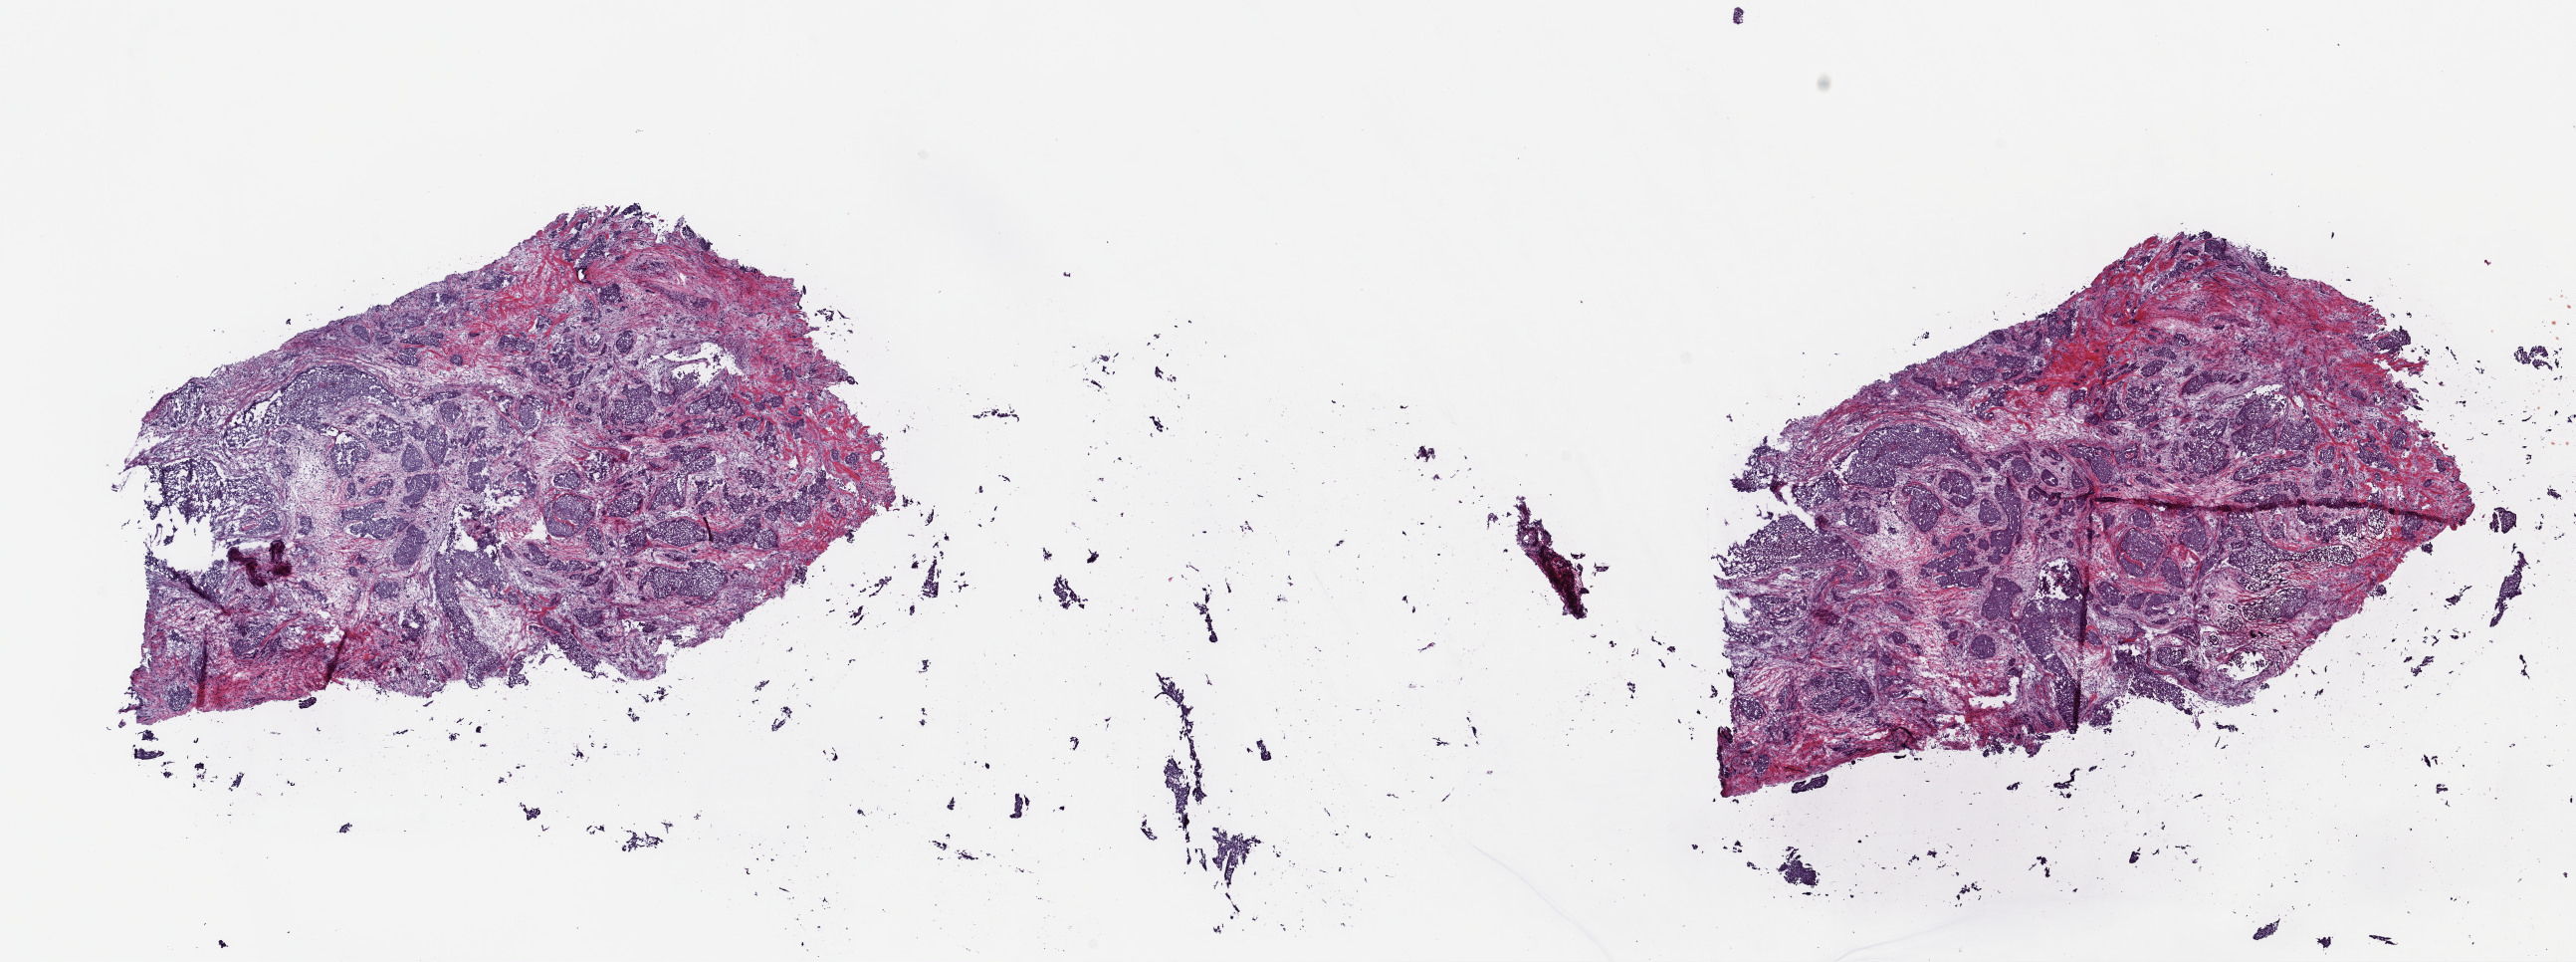
H&E-stained whole-slide image, a low-resolution overview of the entire scanned area, about 20.3 x 7.6 mm. Frozen section. Primary tumour sample from the breast. Patient: female, age at initial diagnosis 36 years. Slide review estimates, as recorded: tumour cells 70%, tumour nuclei 75%, normal cells 0%, stromal cells 30%, necrosis 0%. Inflammatory infiltration, as recorded: lymphocyte infiltration 0%, monocyte infiltration 0%, neutrophil infiltration 0%.
* lymph nodes positive (case pathology): 6 of 18 examined
* AJCC pathologic stage: IIIA
* diagnosis: Infiltrating duct carcinoma, NOS